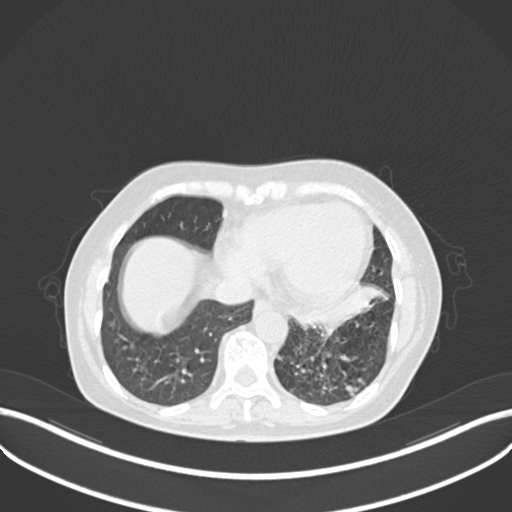
Chest CT, one axial slice. Position 76 of 270 along the scan axis. Lung window (W 1500 / L -600 HU). 1 mm slice thickness. 512 × 512 image matrix, field of view 400 × 400 mm. Patient: female, 63 years. Case-level facts recorded for this patient, not image findings: clinical TNM (as recorded): T1b N0 M0; histopathological grade: G2-3.
Outlined on this slice (bounding box drawn by a radiologist):
- lung tumour (recorded histology: adenocarcinoma): bounding box [x1, y1, x2, y2] px = [292, 284, 391, 333]